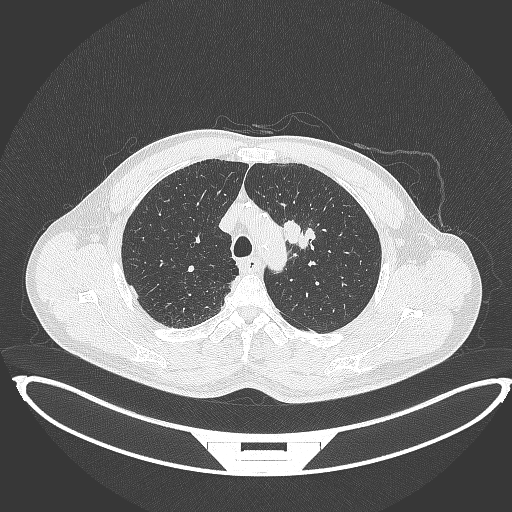
Chest CT, one axial slice. Slice 335 of 395 in the series (ordered by position). Lung window (W 1500 / L -600 HU). 1 mm slice thickness. 512 × 512 image matrix. Patient: male, 60 years. Case-level facts recorded for this patient, not image findings: clinical TNM (as recorded): T2a N0 M0; histopathological grade: G1-G2.
Structures marked on this image (bounding box drawn by a radiologist):
- lung tumour (recorded histology: squamous cell carcinoma): box from (x=282, y=216) to (x=316, y=251) px